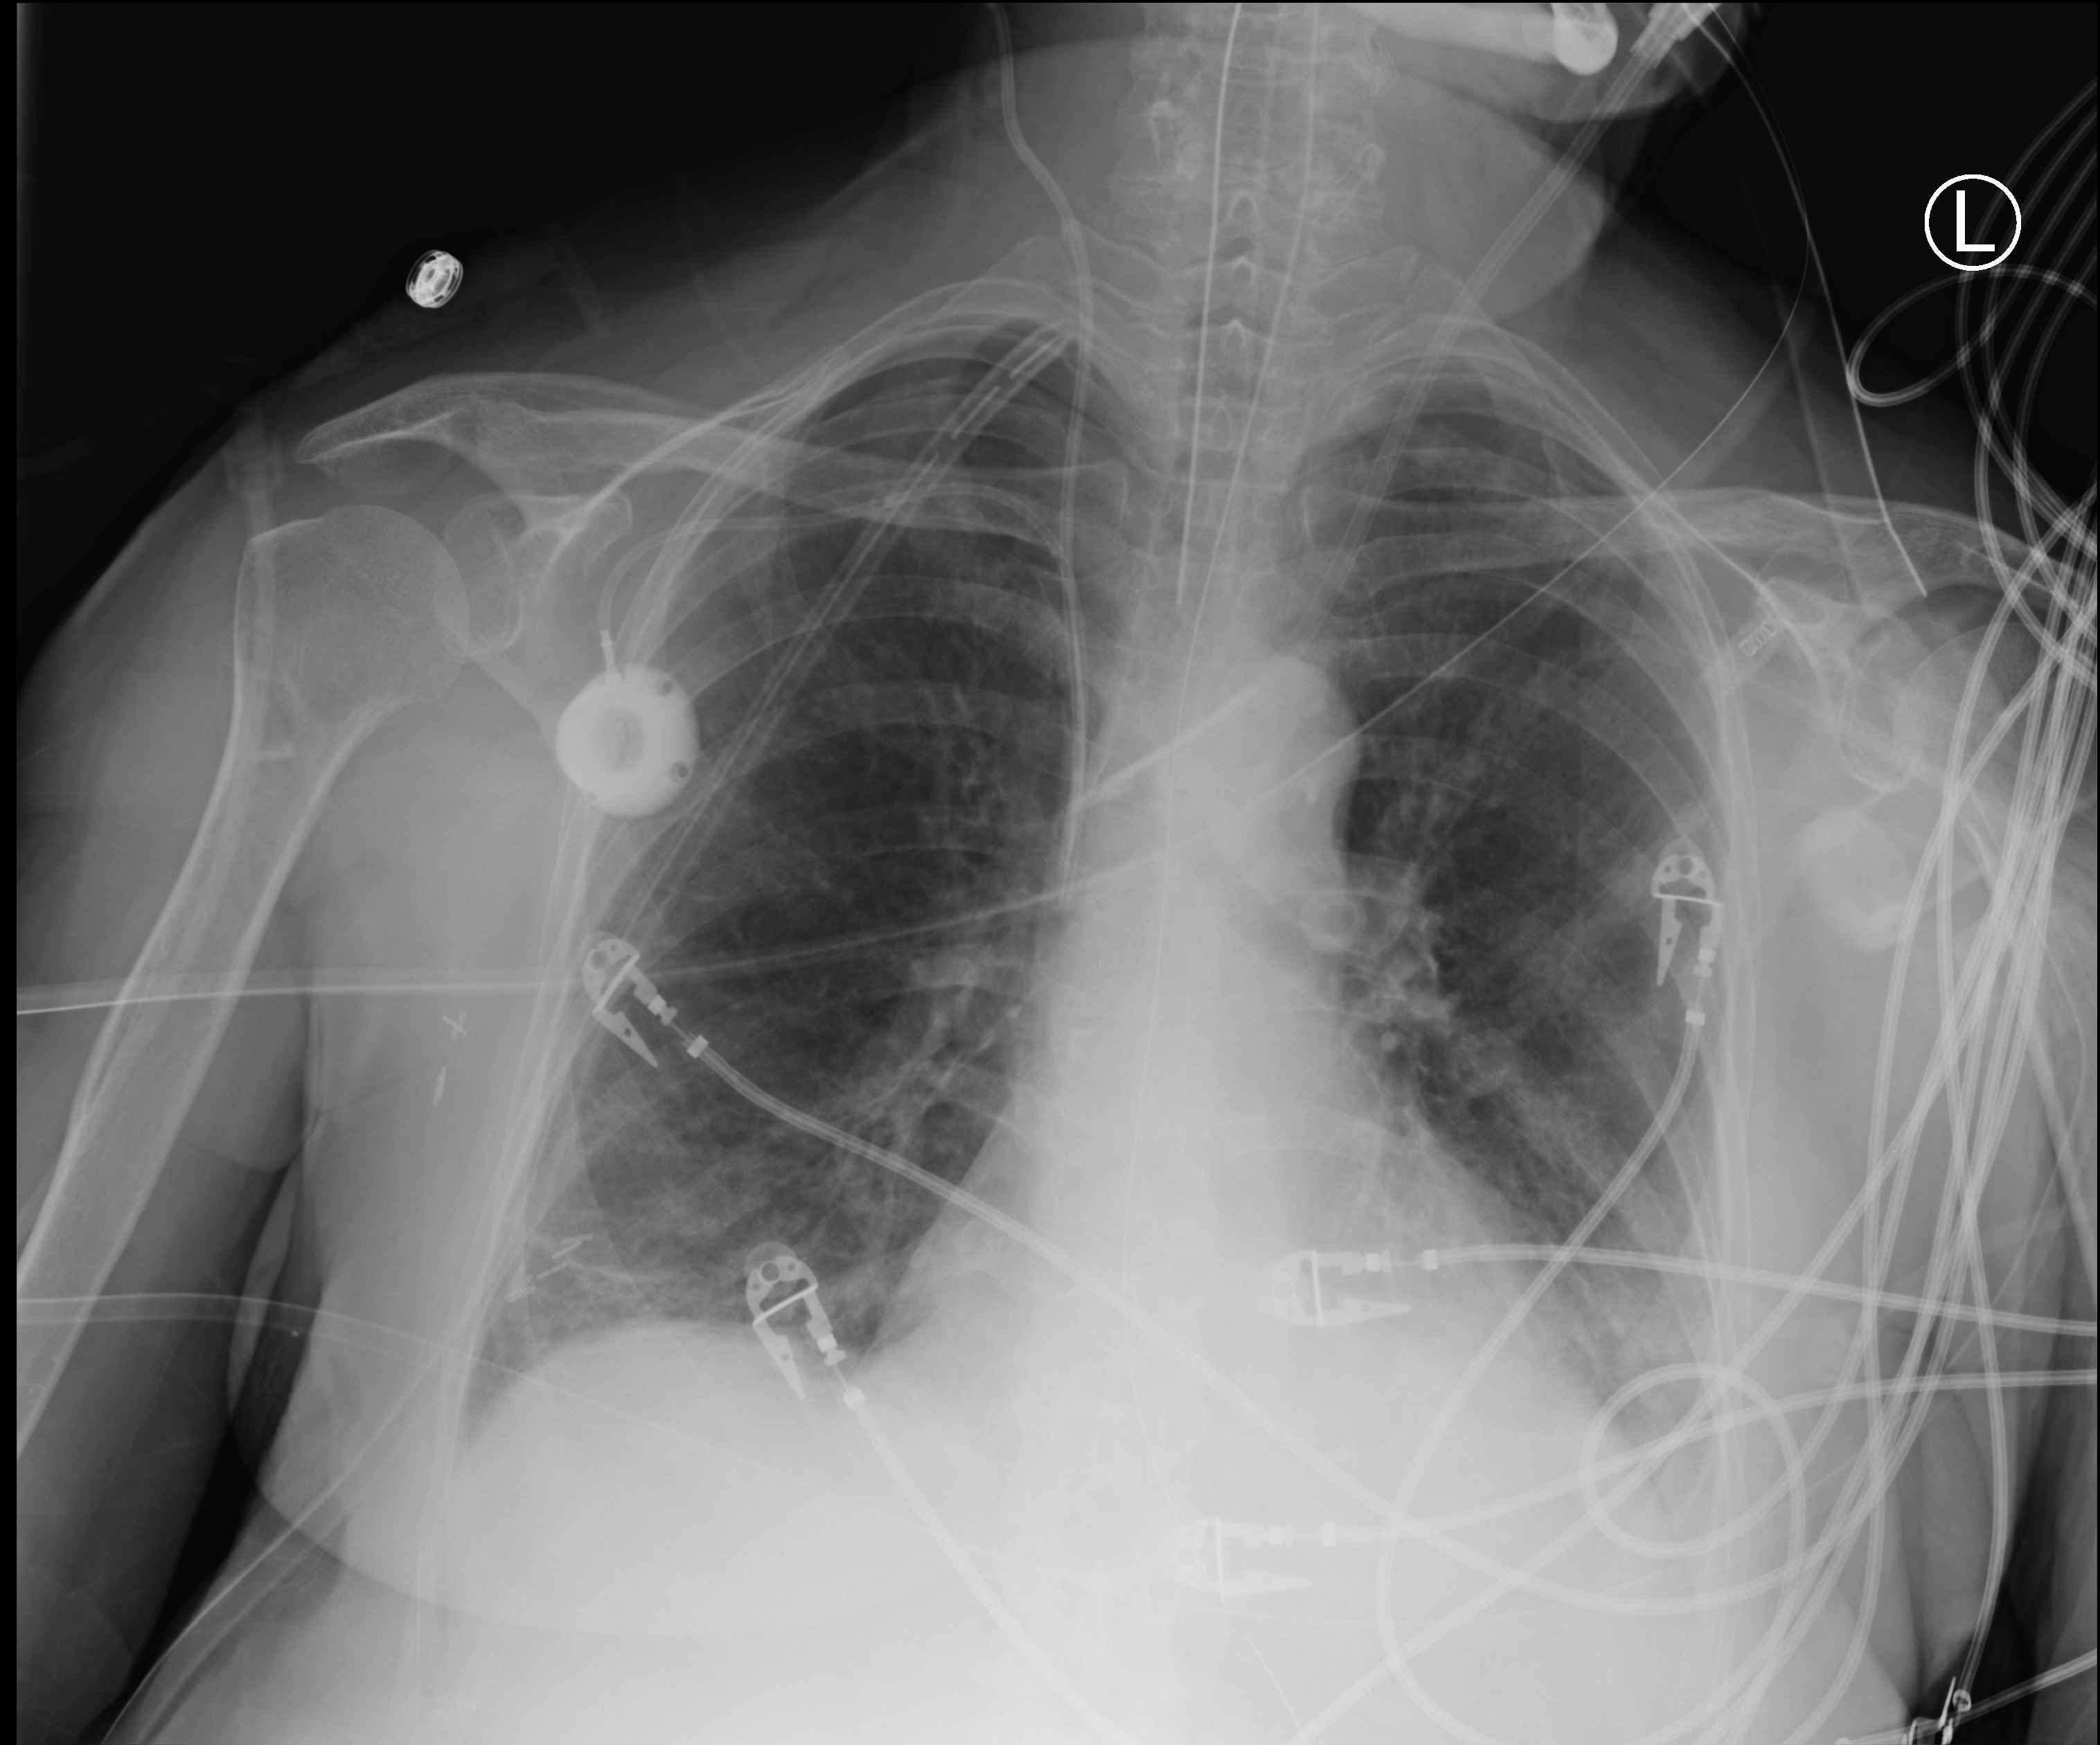
Portable chest radiograph; anteroposterior (AP) projection. Patient hospitalised with COVID-19; female, aged 60–74 years.
Hospital-stay facts (about this admission, not read from this image; timing relative to this image not recorded):
- admitted to intensive care during this hospital stay: yes
- other chronic lung disease (admission record): no
- mechanically ventilated during this hospital stay: yes